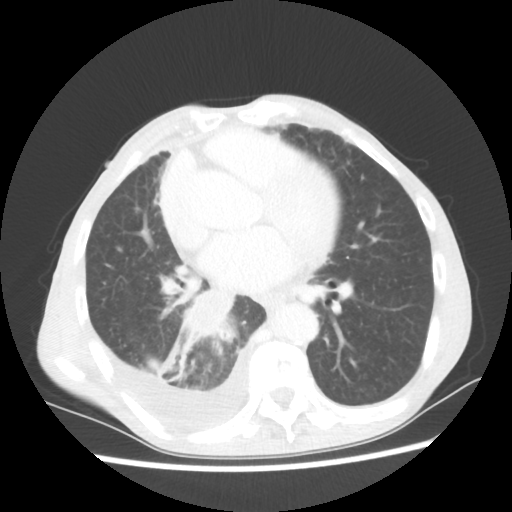
Chest CT, one axial slice; slice 27 of 60 in the series (ordered by position); reconstruction kernel STANDARD; 80 kVp; lung window (W 1500 / L -600 HU); 512 × 512 image matrix. Patient: male, 76 years. Case-level facts recorded for this patient, not image findings: clinical TNM (as recorded): T3 N3 M1a.
Structures marked on this image (rectangle marked by the reading radiologist):
- lung tumour (recorded histology: squamous cell carcinoma): bounding box [x1, y1, x2, y2] px = [158, 287, 240, 382]